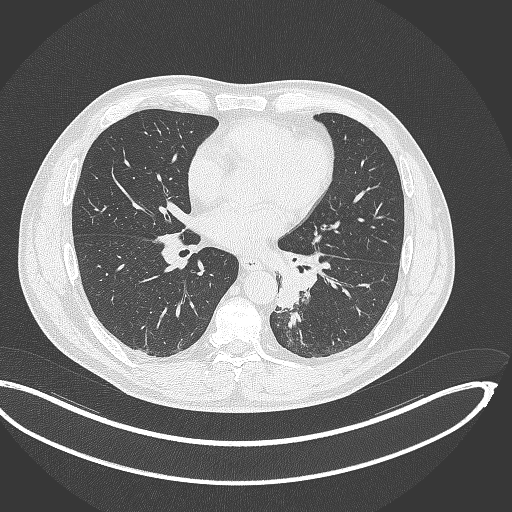
Chest CT, one axial slice. Position 164 of 362 along the scan axis. Reconstruction kernel B70f. Lung window (W 1500 / L -600 HU). 1 mm slice thickness. 512 × 512 image matrix, field of view 442 × 442 mm. Patient: male, 50 years. Case-level facts recorded for this patient, not image findings: clinical TNM (as recorded): T2a N3 M0.
Annotated regions visible in this slice (rectangle marked by the reading radiologist):
- lung tumour (recorded histology: squamous cell carcinoma): bounding box <277,264,317,311> (left, top, right, bottom; pixels)